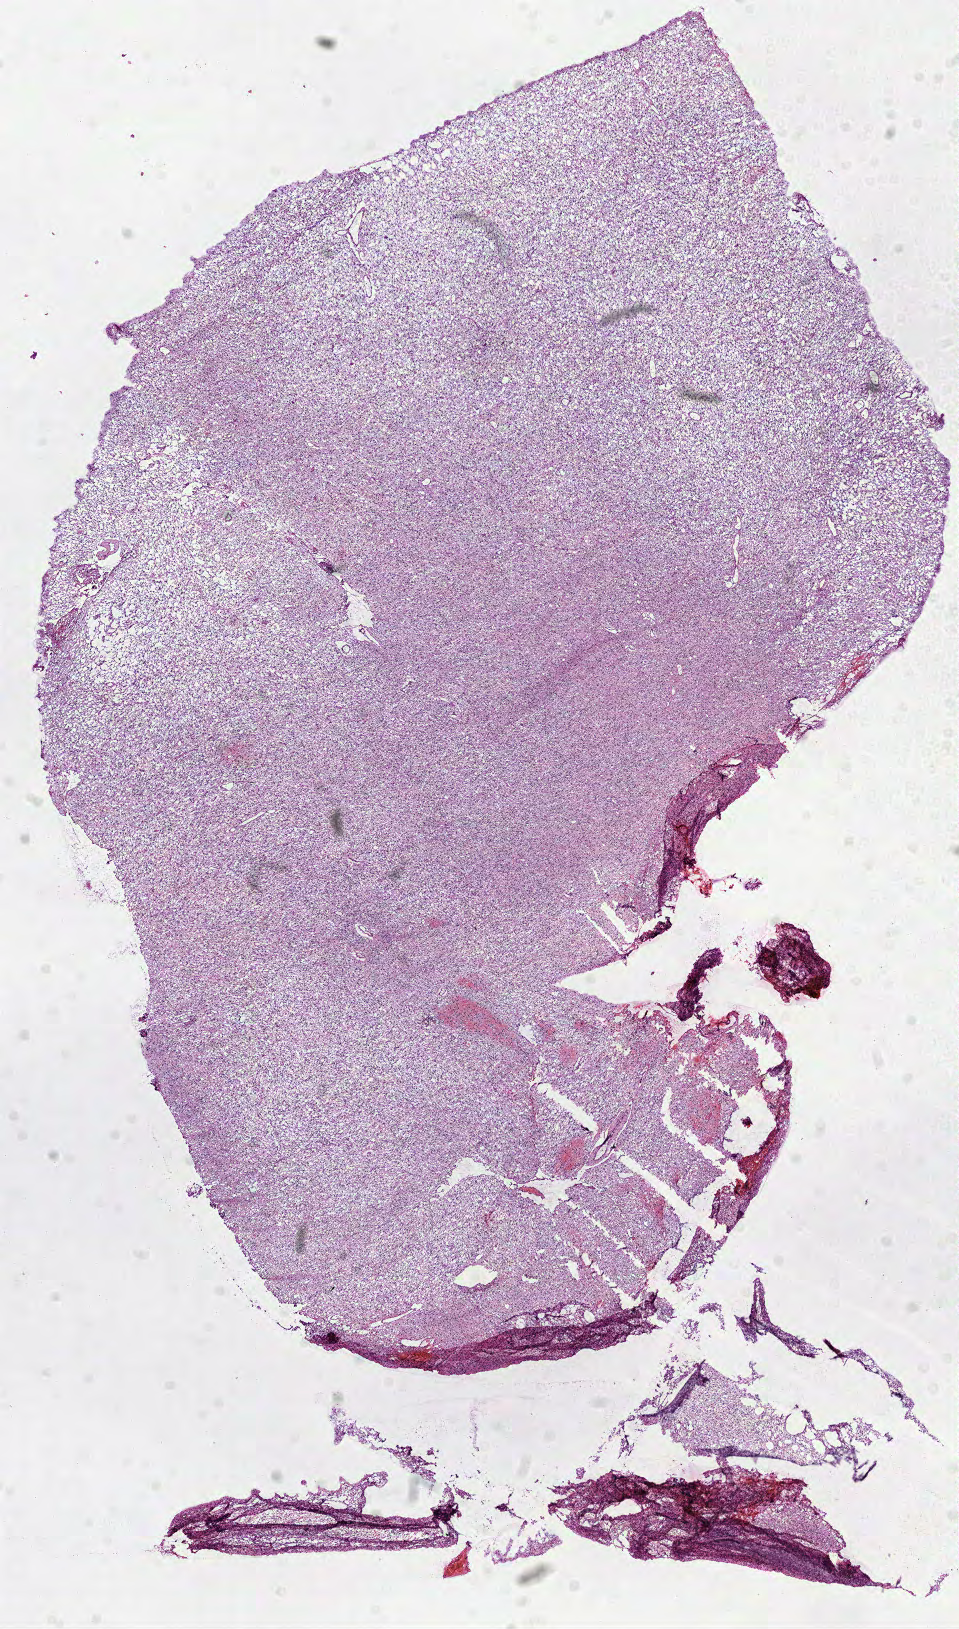
Whole-slide histology image, Hematoxylin and eosin (H&E) stained — low-resolution overview of the scanned area, about 7.7 x 13.1 mm. Frozen section from the top of the tissue portion. Sample: primary tumour, brain. Patient: male, age at initial diagnosis 30 years. Histologic grade: G3 (poorly differentiated). Slide review estimates, as recorded: tumour cells 100%, tumour nuclei 80%, normal cells 0%, stromal cells 0%, necrosis 0%.
Laterality: right. Histologic diagnosis: Oligodendroglioma, anaplastic (cerebrum).